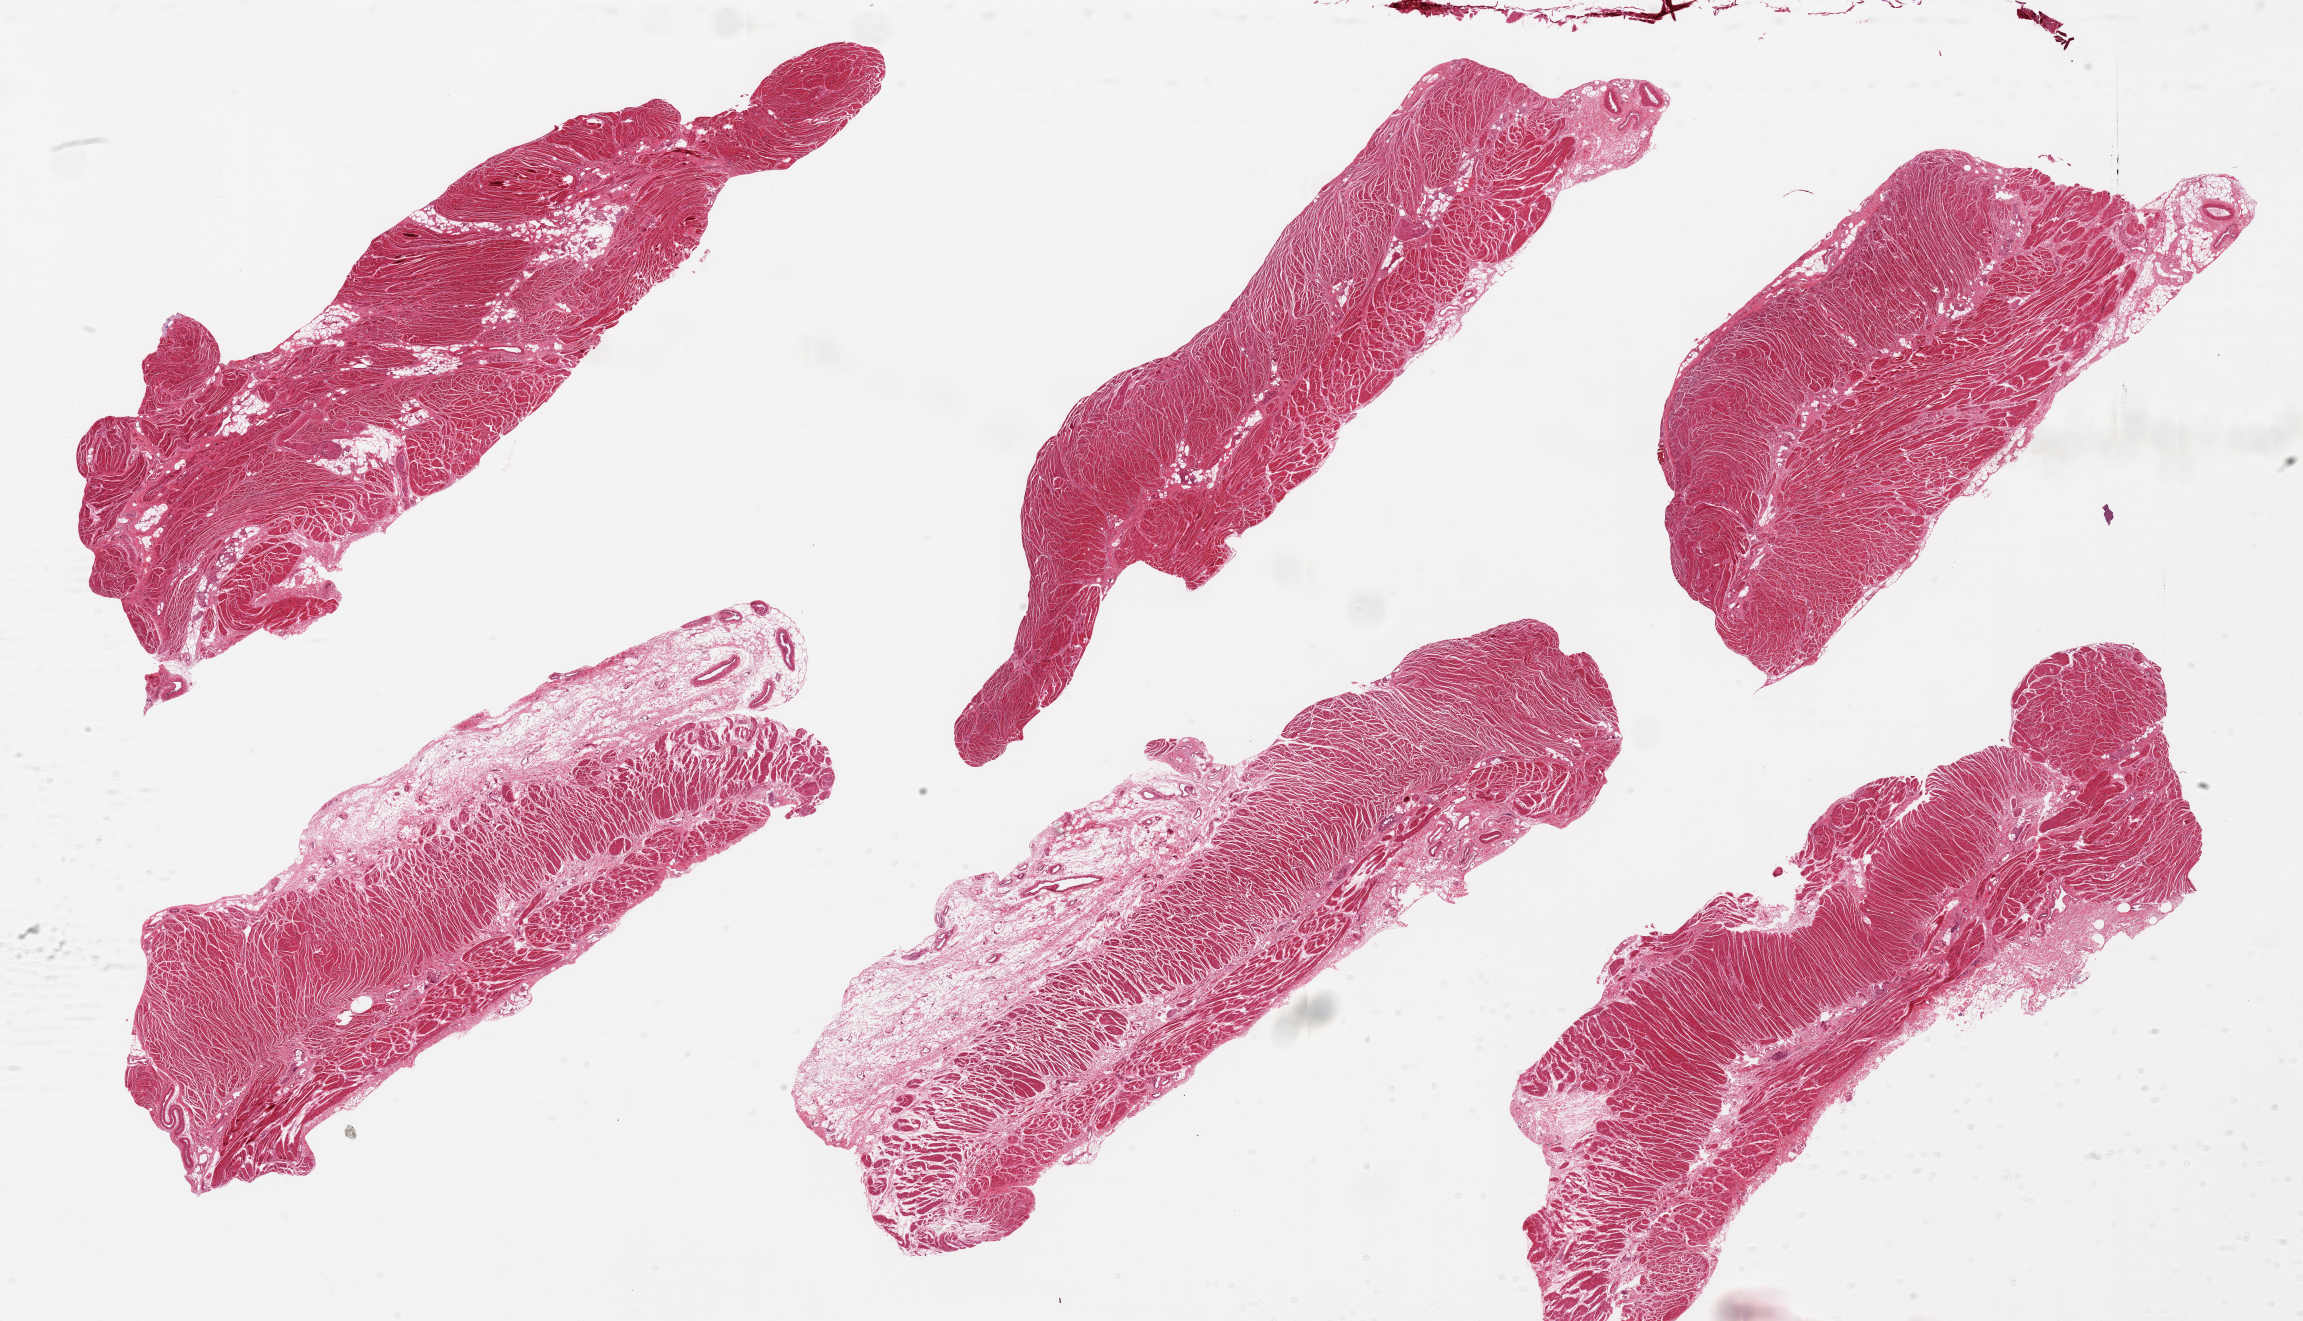
H&E whole-slide image, whole scanned area (about 36.4 x 20.9 mm, acquisition: 20x scan) shown as a low-resolution overview; PAXgene-fixed, paraffin-embedded tissue; target tissue: gastroesophageal junction; tissue donor sample. Donor sex: male.
Reviewer comment on this tissue sample: 6 pieces, well trimmed of mucosa.